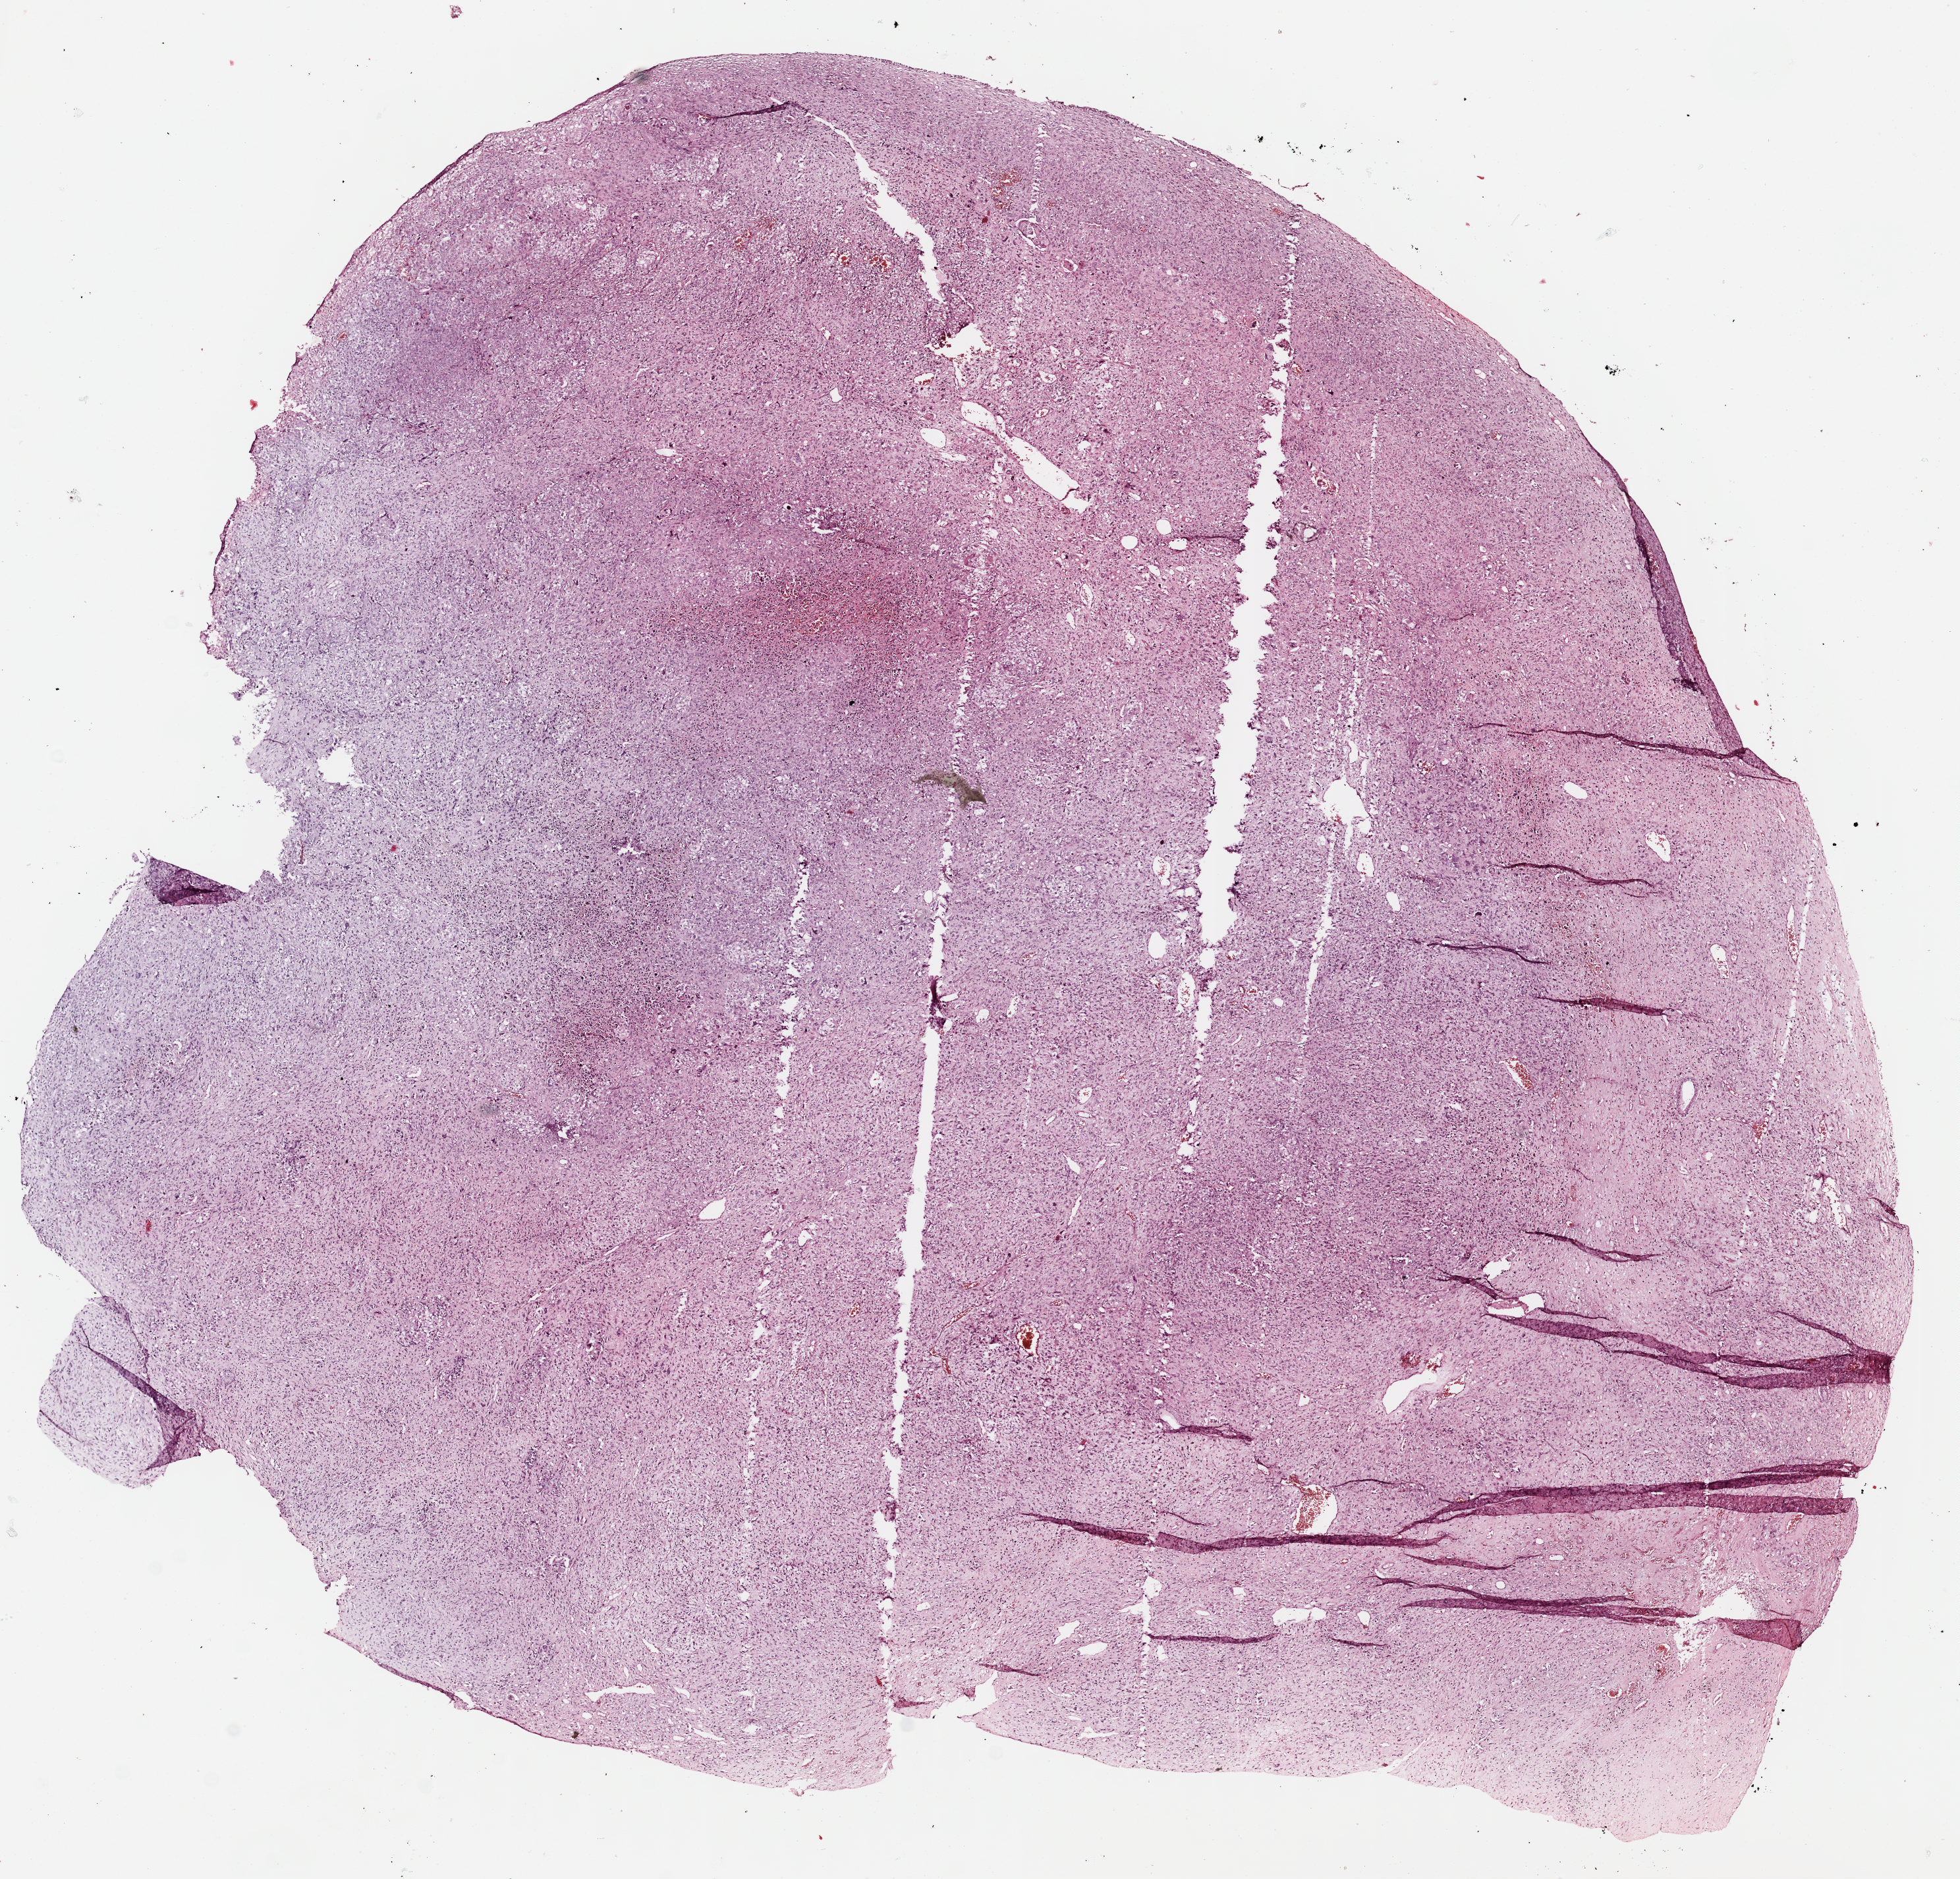
Digitized H&E tissue section (whole slide) — a low-resolution overview of the entire scanned area, about 11.7 x 11.2 mm. Formalin-fixed paraffin-embedded (FFPE) diagnostic section. Uterus, primary tumour sample. Patient: female, age at initial diagnosis 55 years.
• pathologic diagnosis: Mullerian mixed tumor (endometrium)
• FIGO stage: IB